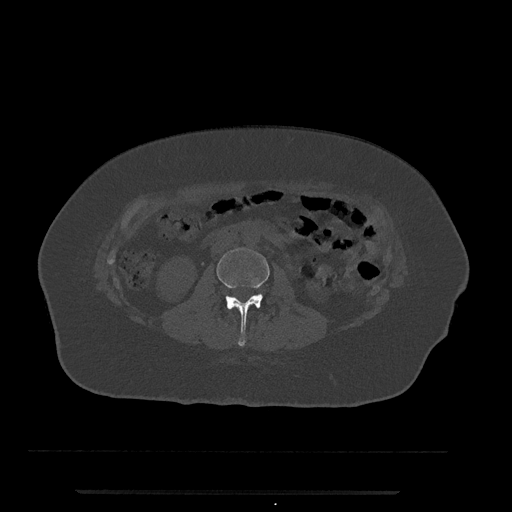
CT including the spine, one axial slice. Reconstruction kernel Br40s/3. 120 kVp. Bone window (W 1800 / L 400 HU). 512 × 512 image matrix, field of view 440 × 440 mm. Female patient, age 51 years. From the clinical record (not read from this slice): primary cancer: neuro; vertebrae with lytic lesions (as recorded): T8.
Outlined on this slice (semi-automatic segmentation, software-assisted and operator-edited):
- L2 vertebra: box from (x=217, y=248) to (x=270, y=346) px